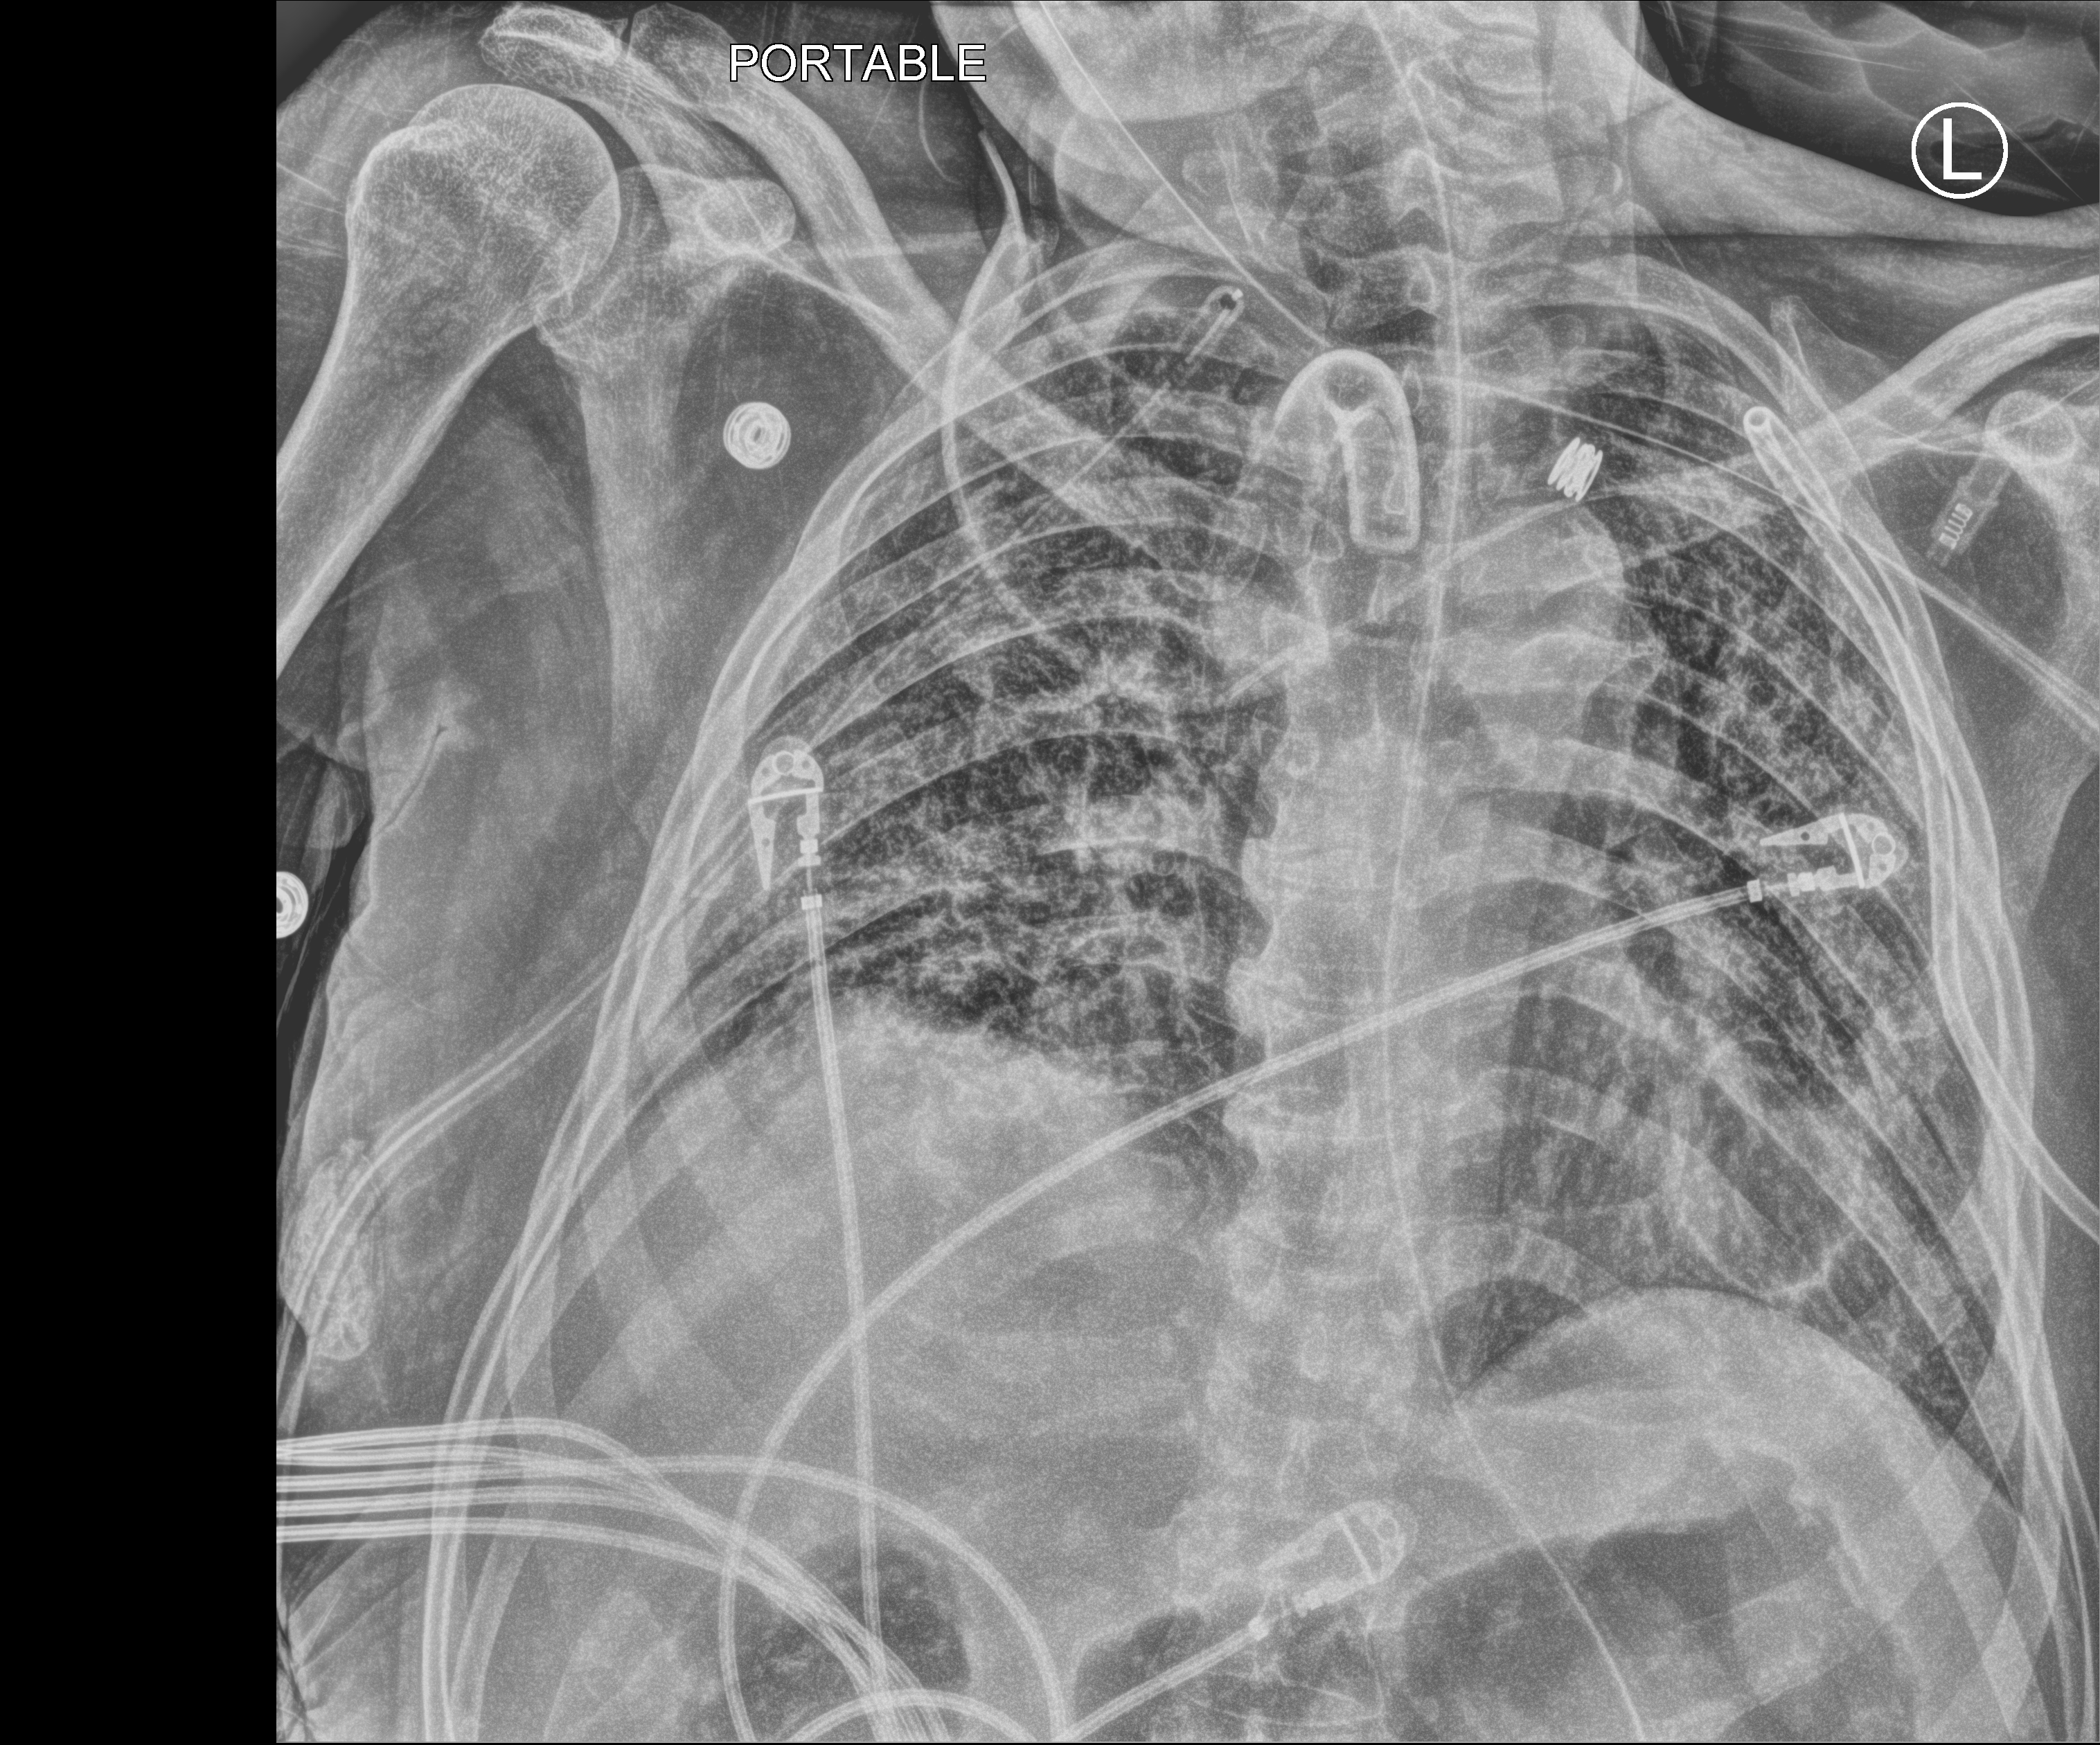
Portable chest radiograph. Patient hospitalised with COVID-19; male, aged 18–59 years.
From the hospital-stay record, not from the radiograph (when in the stay this image was taken is not recorded): admitted to intensive care during this hospital stay: yes; length of hospital stay: 83 days; mechanically ventilated during this hospital stay: yes.